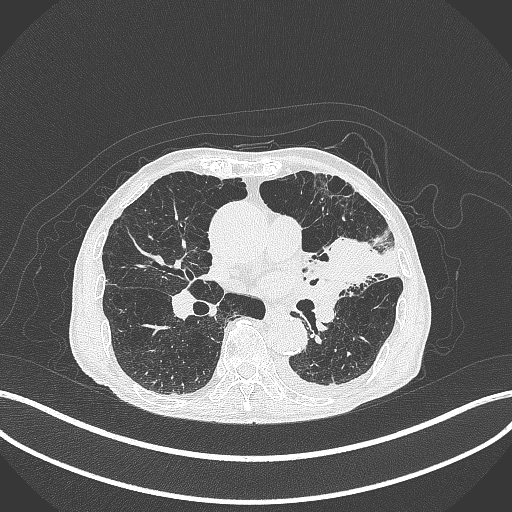
Chest CT, one axial slice; slice 197 of 385 in the series (ordered by position); reconstruction kernel B70f; 120 kVp; lung window (W 1500 / L -600 HU); 1 mm slice thickness; 512 × 512 image matrix, field of view 400 × 400 mm. Patient: male, 90 years or older. Case-level facts recorded for this patient, not image findings: clinical TNM (as recorded): T2b N1 M0.
Outlined on this slice (bounding box drawn by a radiologist):
- lung tumour (recorded histology: squamous cell carcinoma): box from (x=317, y=233) to (x=383, y=288) px